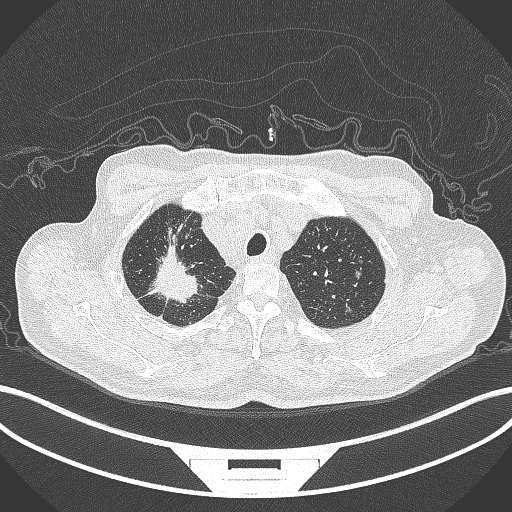
Chest CT, one axial slice. Slice 331 of 407 in the series (ordered by position). Reconstruction kernel B70f. Lung window (W 1500 / L -600 HU). 1 mm slice thickness. 512 × 512 image matrix, field of view 400 × 400 mm. Male patient, age 69 years. From the clinical record (not read from this slice): clinical TNM (as recorded): T1c N1 M1.
Structures marked on this image (bounding box drawn by a radiologist):
- lung tumour (recorded histology: adenocarcinoma): bounding box (x1, y1, x2, y2) in pixels: (143, 243, 206, 307)